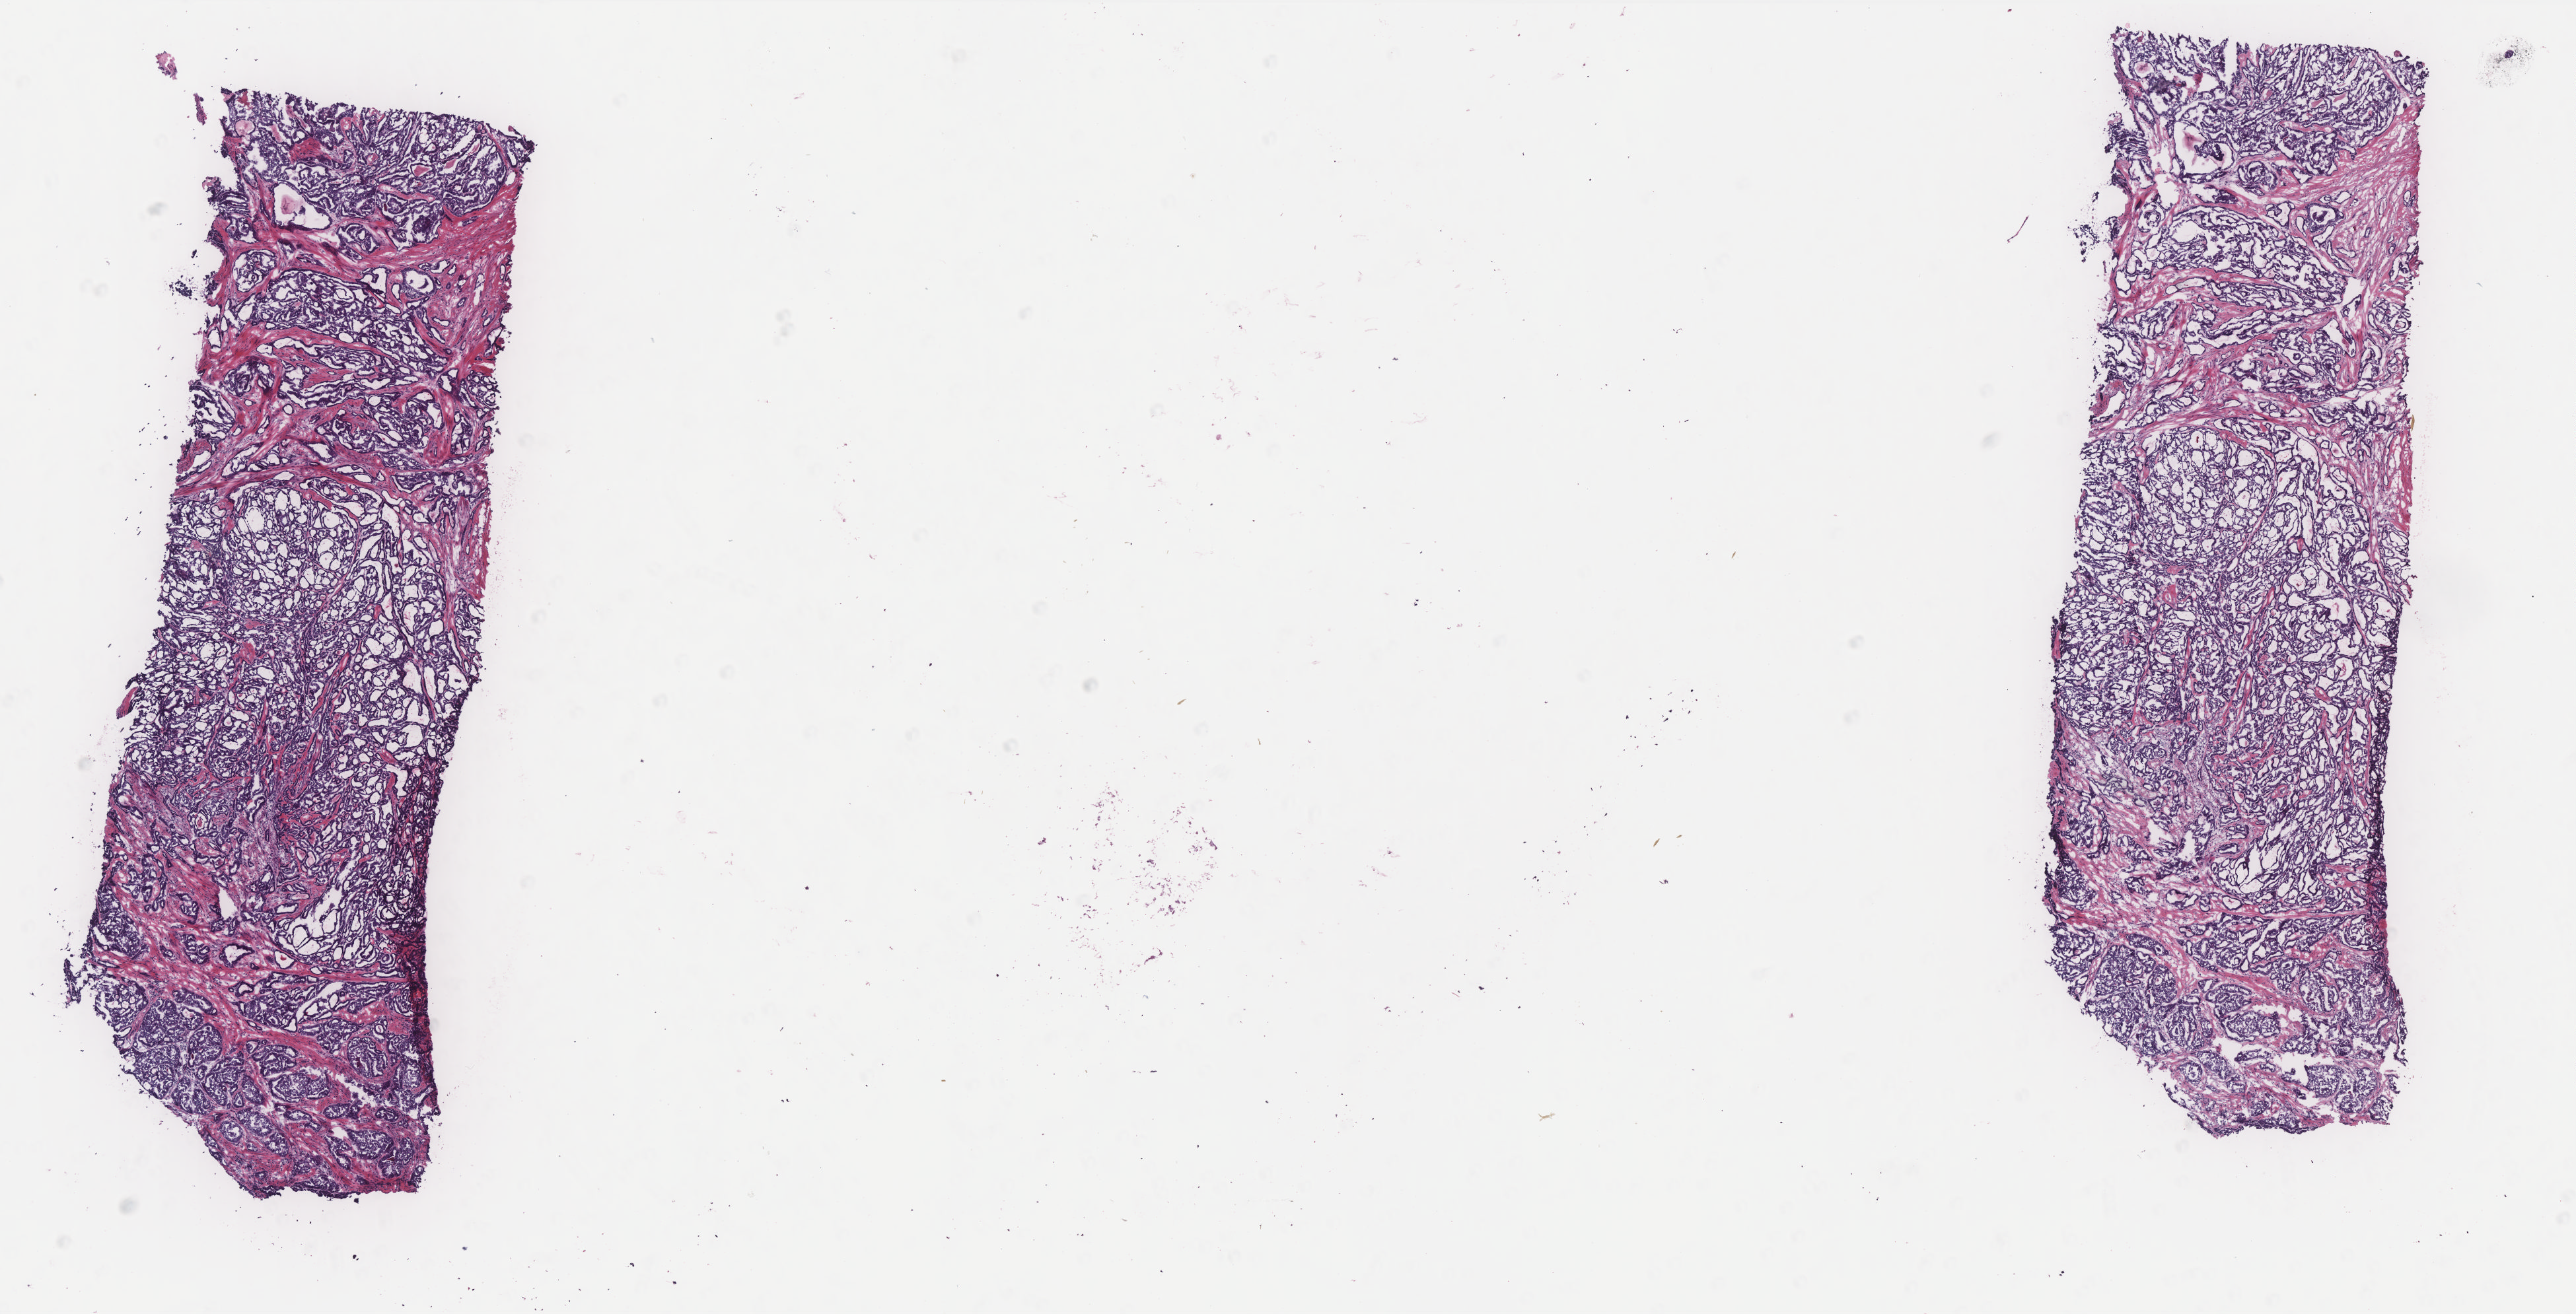
Digitized H&E tissue section (whole slide) — low-resolution overview of the scanned area, about 15.6 x 8.0 mm. Frozen section from the bottom of the tissue portion. Thyroid, primary tumour sample. Patient: male, age at initial diagnosis 66 years. Composition of this section per pathologist review: tumour cells 85%, tumour nuclei 85%, normal cells 0%, stromal cells 15%, necrosis 0%. Infiltration values recorded for this section: lymphocyte infiltration 1%, monocyte infiltration 0%, neutrophil infiltration 0%.
* lymph nodes positive (case pathology): 5 of 6 examined
* histologic diagnosis: Papillary adenocarcinoma, NOS (thyroid gland)
* laterality: right
* AJCC pathologic stage: IVA (7th edition)